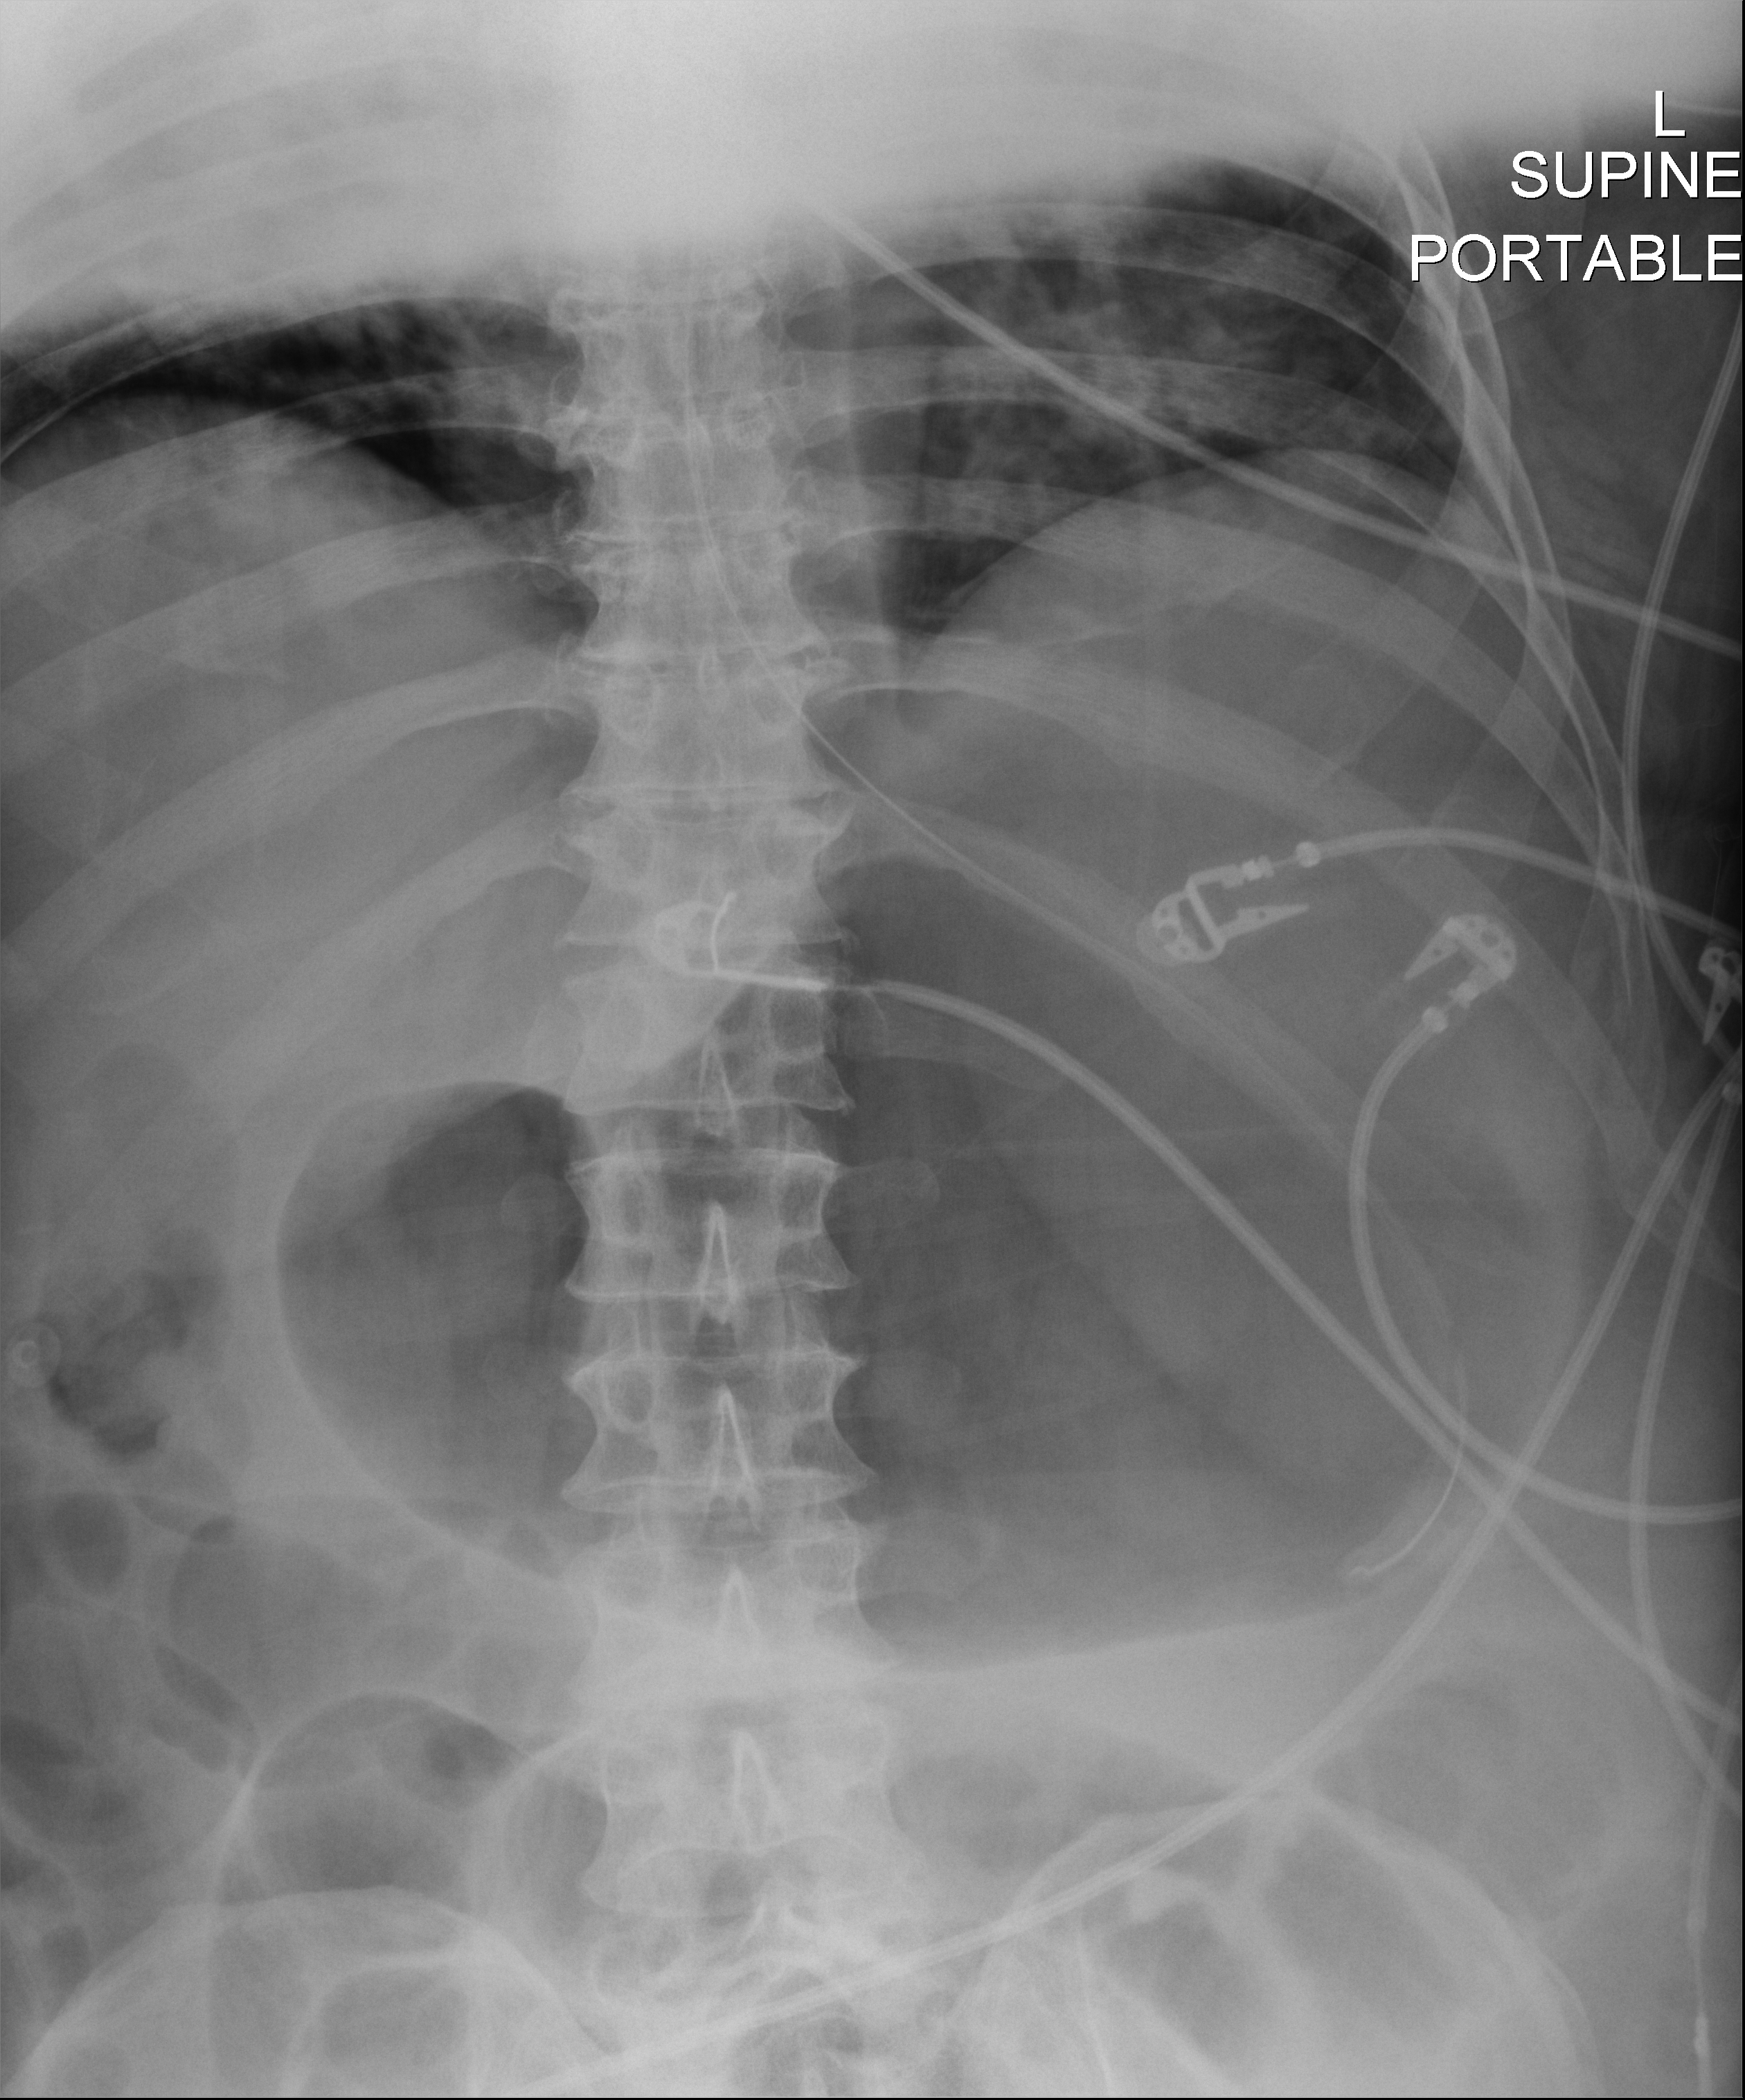
Bedside abdomen radiograph (digital radiography), anteroposterior (AP) projection. Patient hospitalised with COVID-19; male, aged 18–59 years.
From the hospital-stay record, not from the radiograph (when in the stay this image was taken is not recorded):
- admitted to intensive care during this hospital stay: yes
- length of hospital stay: 28 days
- mechanically ventilated during this hospital stay: yes